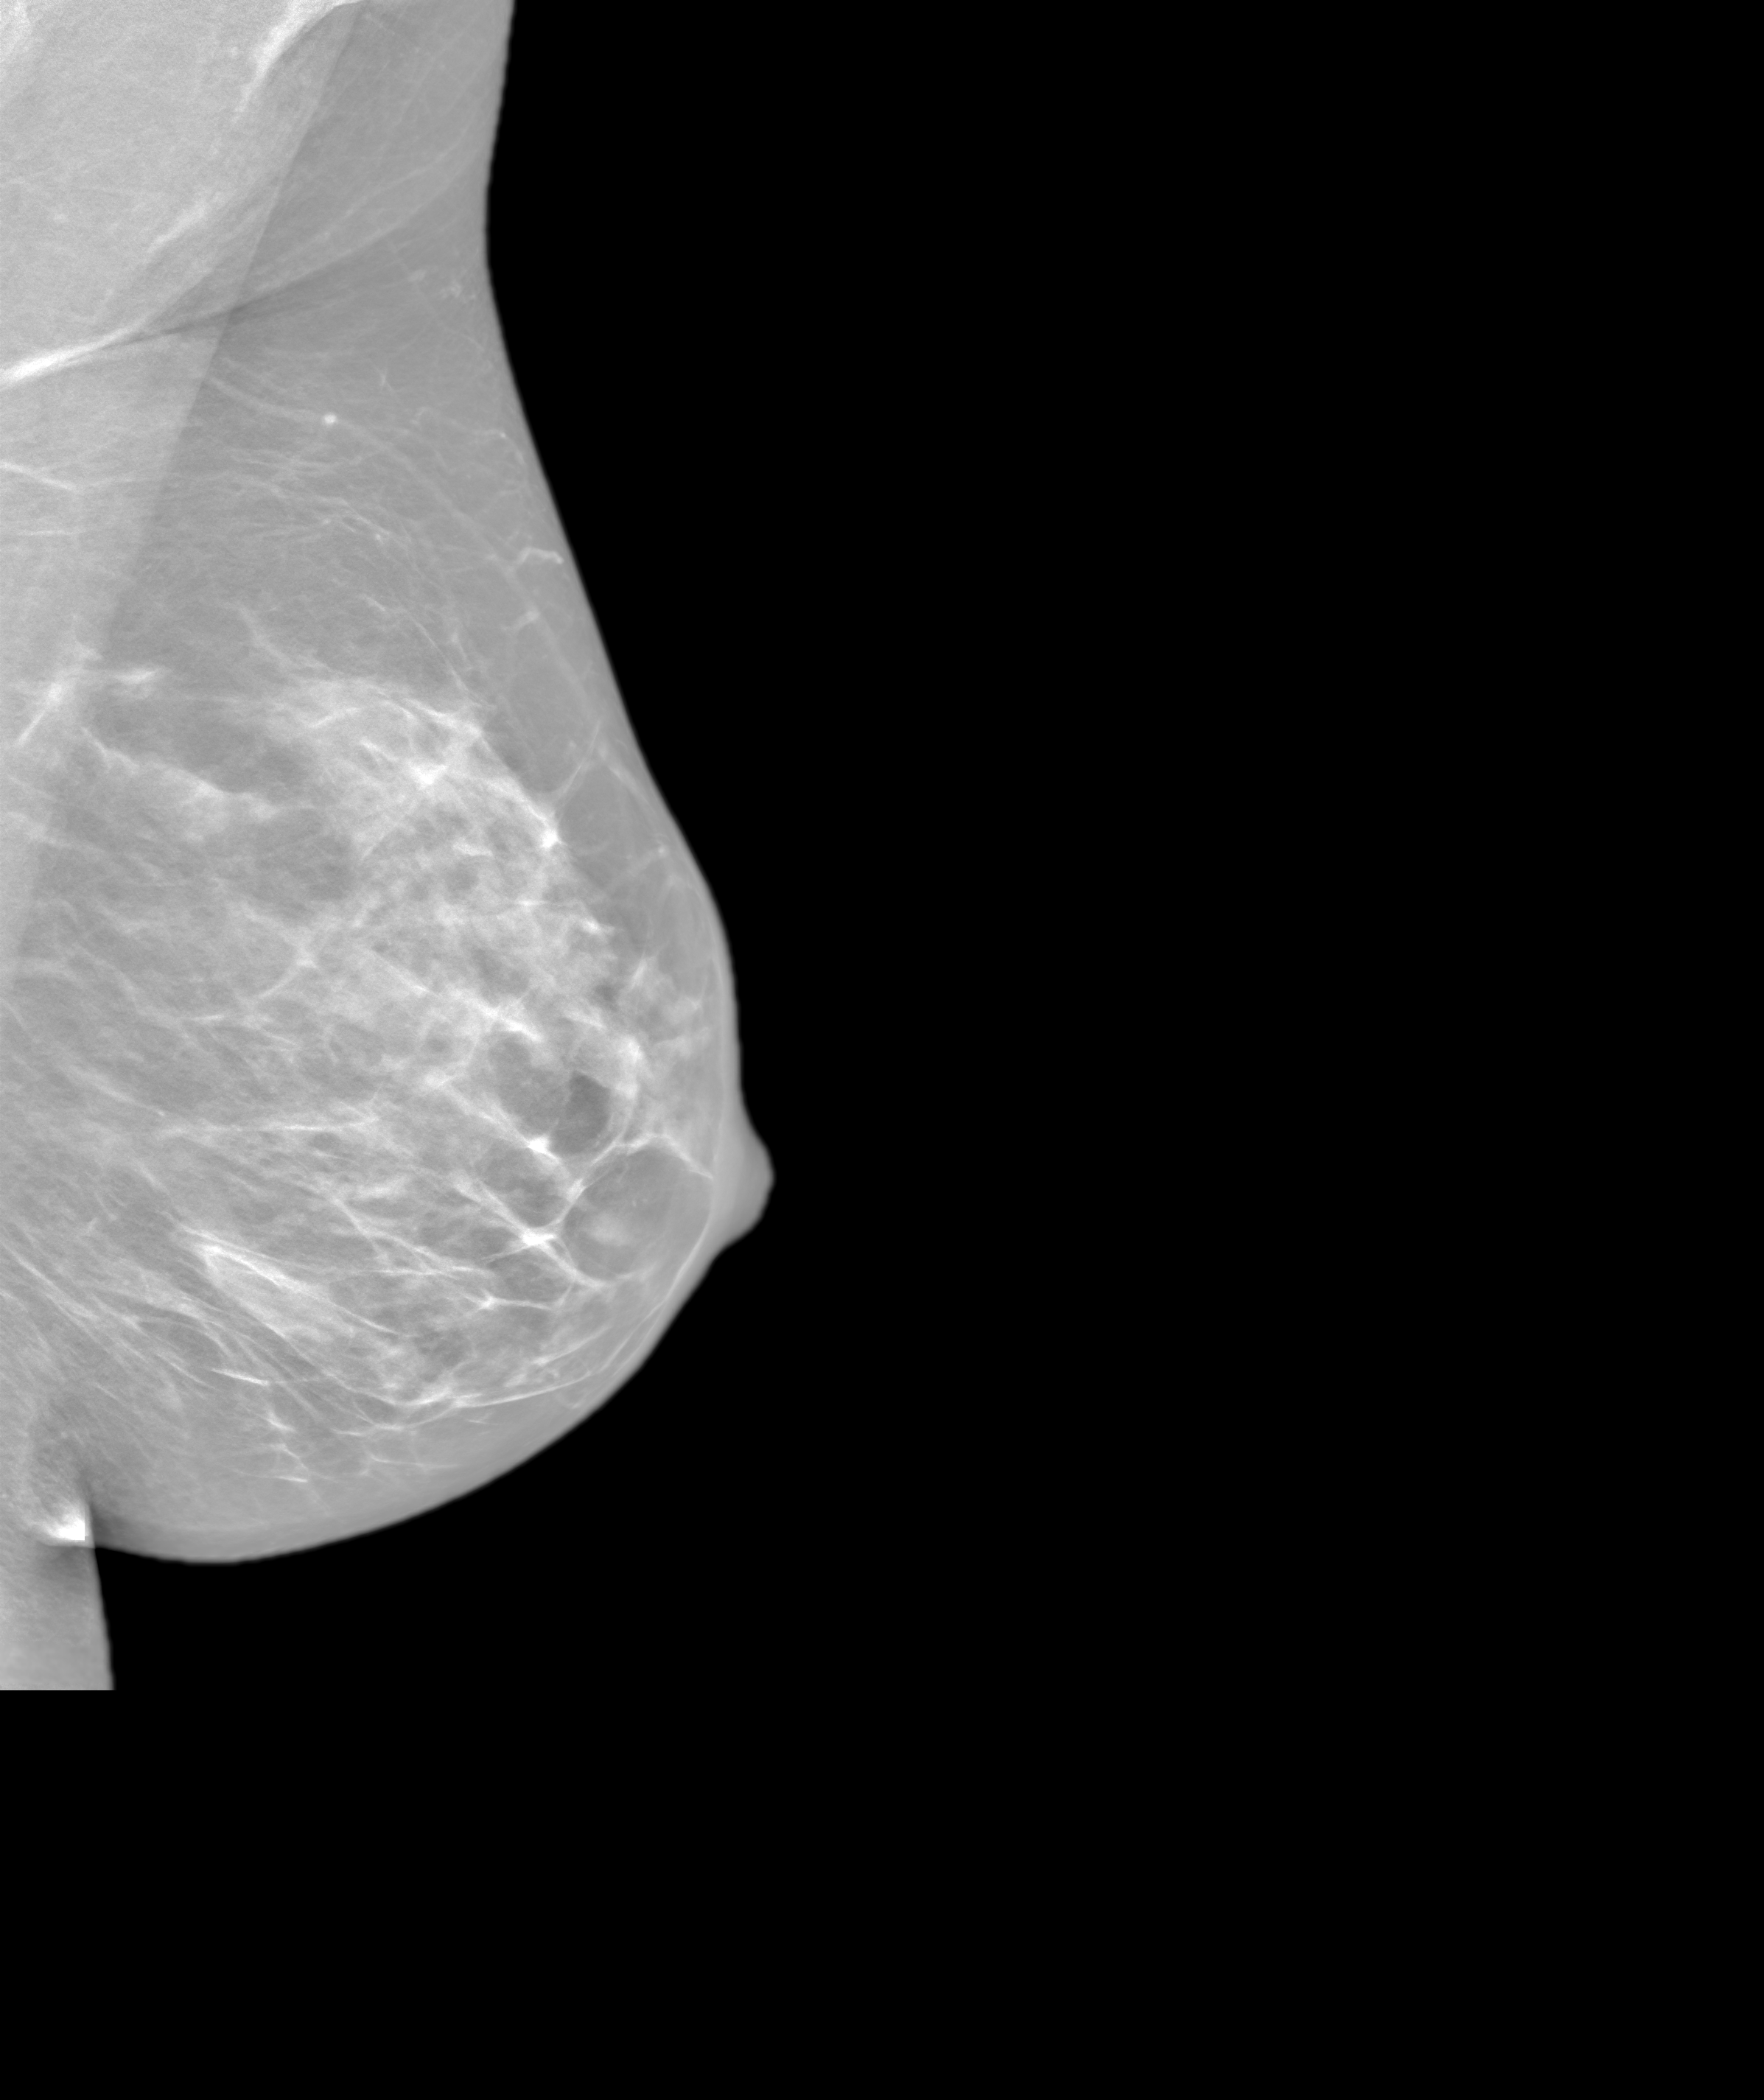
Annual screening mammography examination. Female patient, age 46 years.
Image type: synthesized 2-D view from tomosynthesis. Breast: left. Projection: mediolateral oblique (MLO) view.